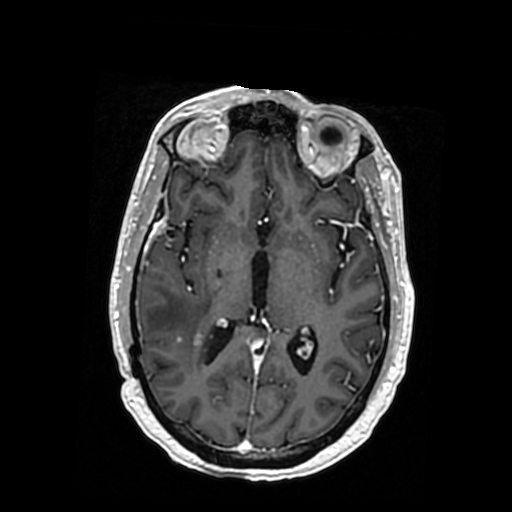
Brain MRI from a brain-tumour surgery series, one axial slice. Position 186 of 364 along the scan axis. T1-weighted post-contrast. 512 × 512 image matrix, field of view 260 × 260 mm. From the clinical record (not read from this slice): histopathology: Oligodendroglioma; WHO grade: 3; IDH mutation: yes.
Annotated regions visible in this slice (outlined manually by an expert reader):
- tumour: bounding box <180,331,208,342> (left, top, right, bottom; pixels)